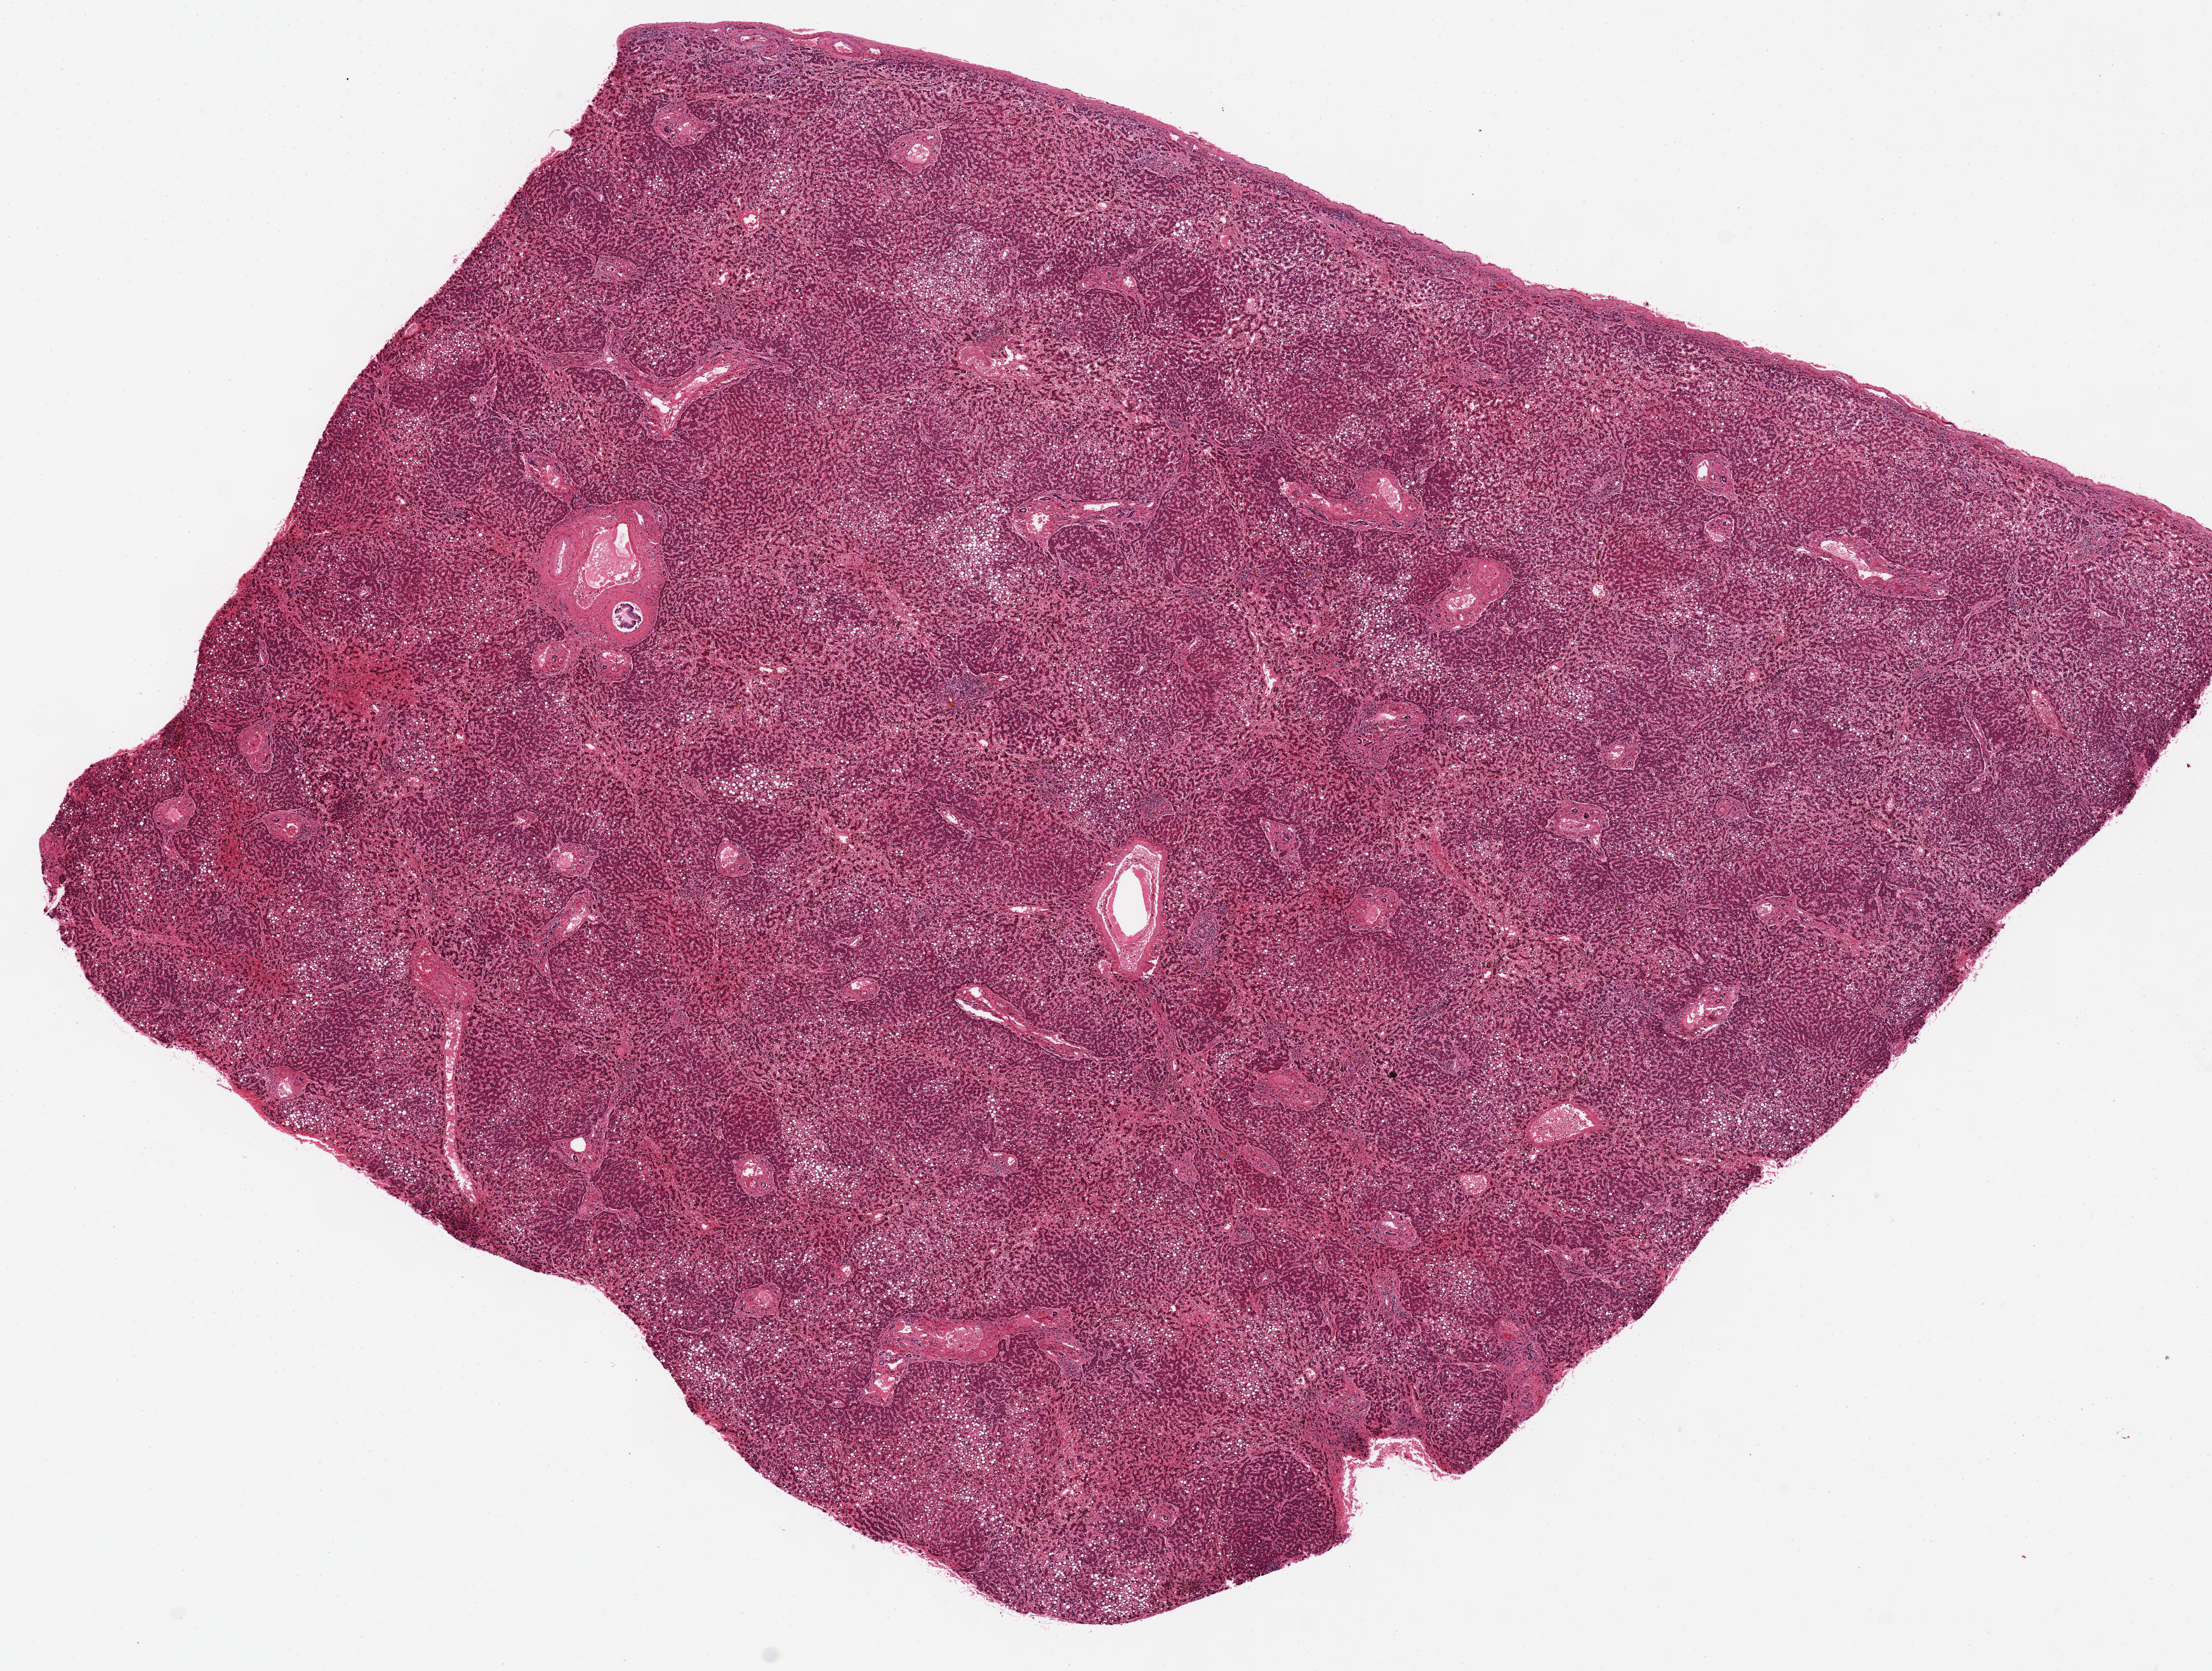
Hematoxylin and eosin (H&E) whole-slide image, low-resolution overview of the scanned area, about 13.8 x 10.4 mm (slide scanned at 20x). PAXgene-fixed, paraffin-embedded tissue. Target tissue: liver. Donor tissue sample. Donor: female.
Review note (as recorded): 40-50% macrovesicular steatosis; mild chronic passive congestion.